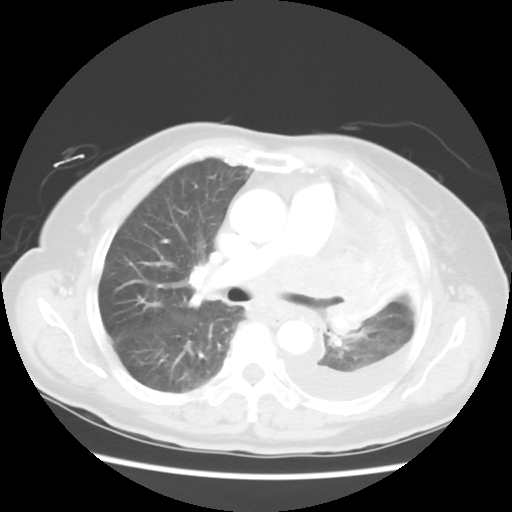
Chest CT, one axial slice. Slice 33 of 52 in the series (ordered by position). Reconstruction kernel STANDARD. 120 kVp. Lung window (W 1500 / L -600 HU). 5 mm slice thickness. 512 × 512 image matrix, field of view 336 × 336 mm. Patient: female, 72 years. Case-level facts recorded for this patient, not image findings: clinical TNM (as recorded): T4 N3 M1b; histopathological grade: G3.
Structures marked on this image (rectangle marked by the reading radiologist):
- lung tumour (recorded histology: large cell carcinoma): bounding box <309,249,397,351> (left, top, right, bottom; pixels)